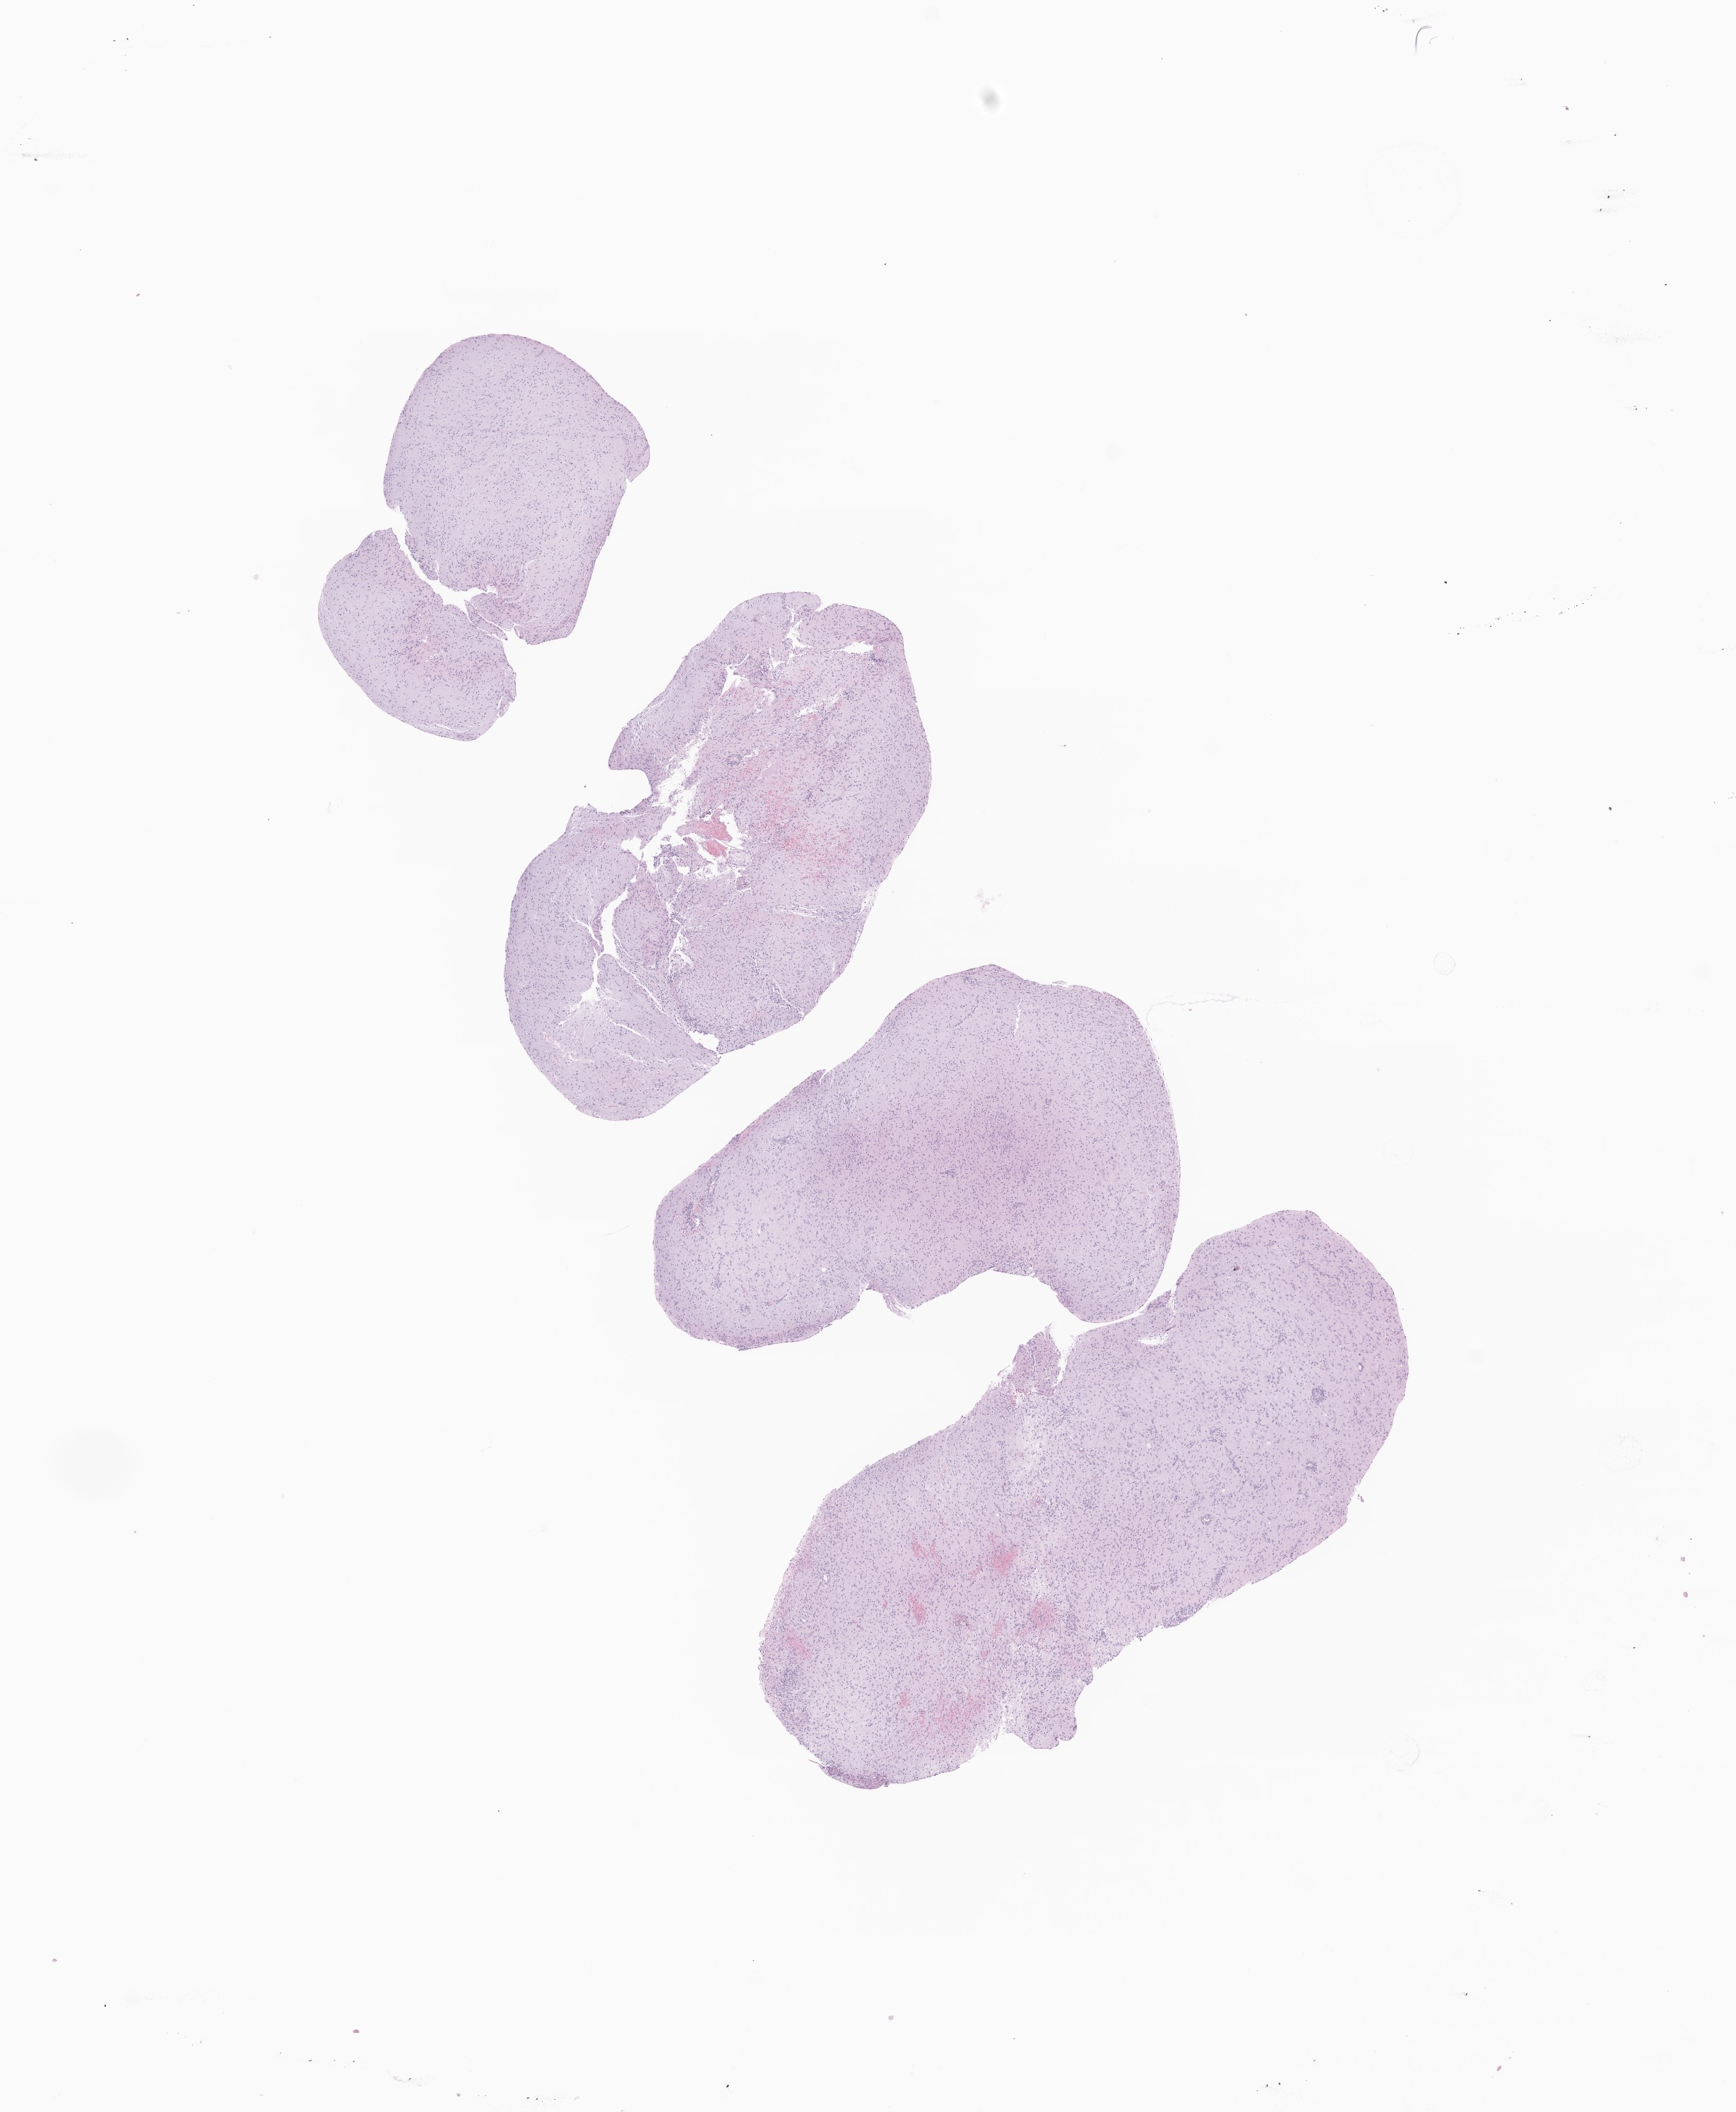
Haematoxylin and eosin whole-slide image of tumor tissue from the cerebrum — shown as a low-resolution overview of the whole scanned area (about 10.3 x 12.5 mm), formalin-fixed paraffin-embedded section. Patient: male, age 115 months (9 years 7 months).
Diagnosis: Neoplasm, uncertain whether benign or malignant.